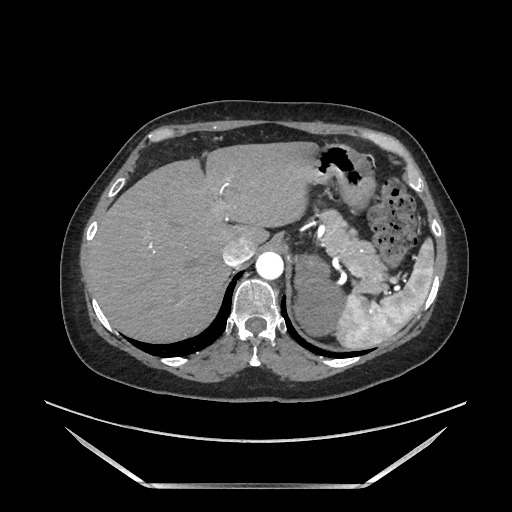
Contrast-enhanced abdominal CT, one axial slice. Slice 142 of 205 in the series (ordered by position). Soft-tissue window (W 400 / L 40 HU). 1.25 mm slice thickness. 512 × 512 image matrix, field of view 440 × 440 mm. Female patient. From the clinical record (not read from this slice): diagnosis: adrenocortical carcinoma; tumour side: left adrenal; tumour size at pathology: 12.5 cm; Ki-67 index: 39 %; stage (as recorded): 3.
Annotated regions visible in this slice (semi-automatically segmented with operator editing):
- mass: bounding box (x1, y1, x2, y2) in pixels: (294, 254, 346, 336)